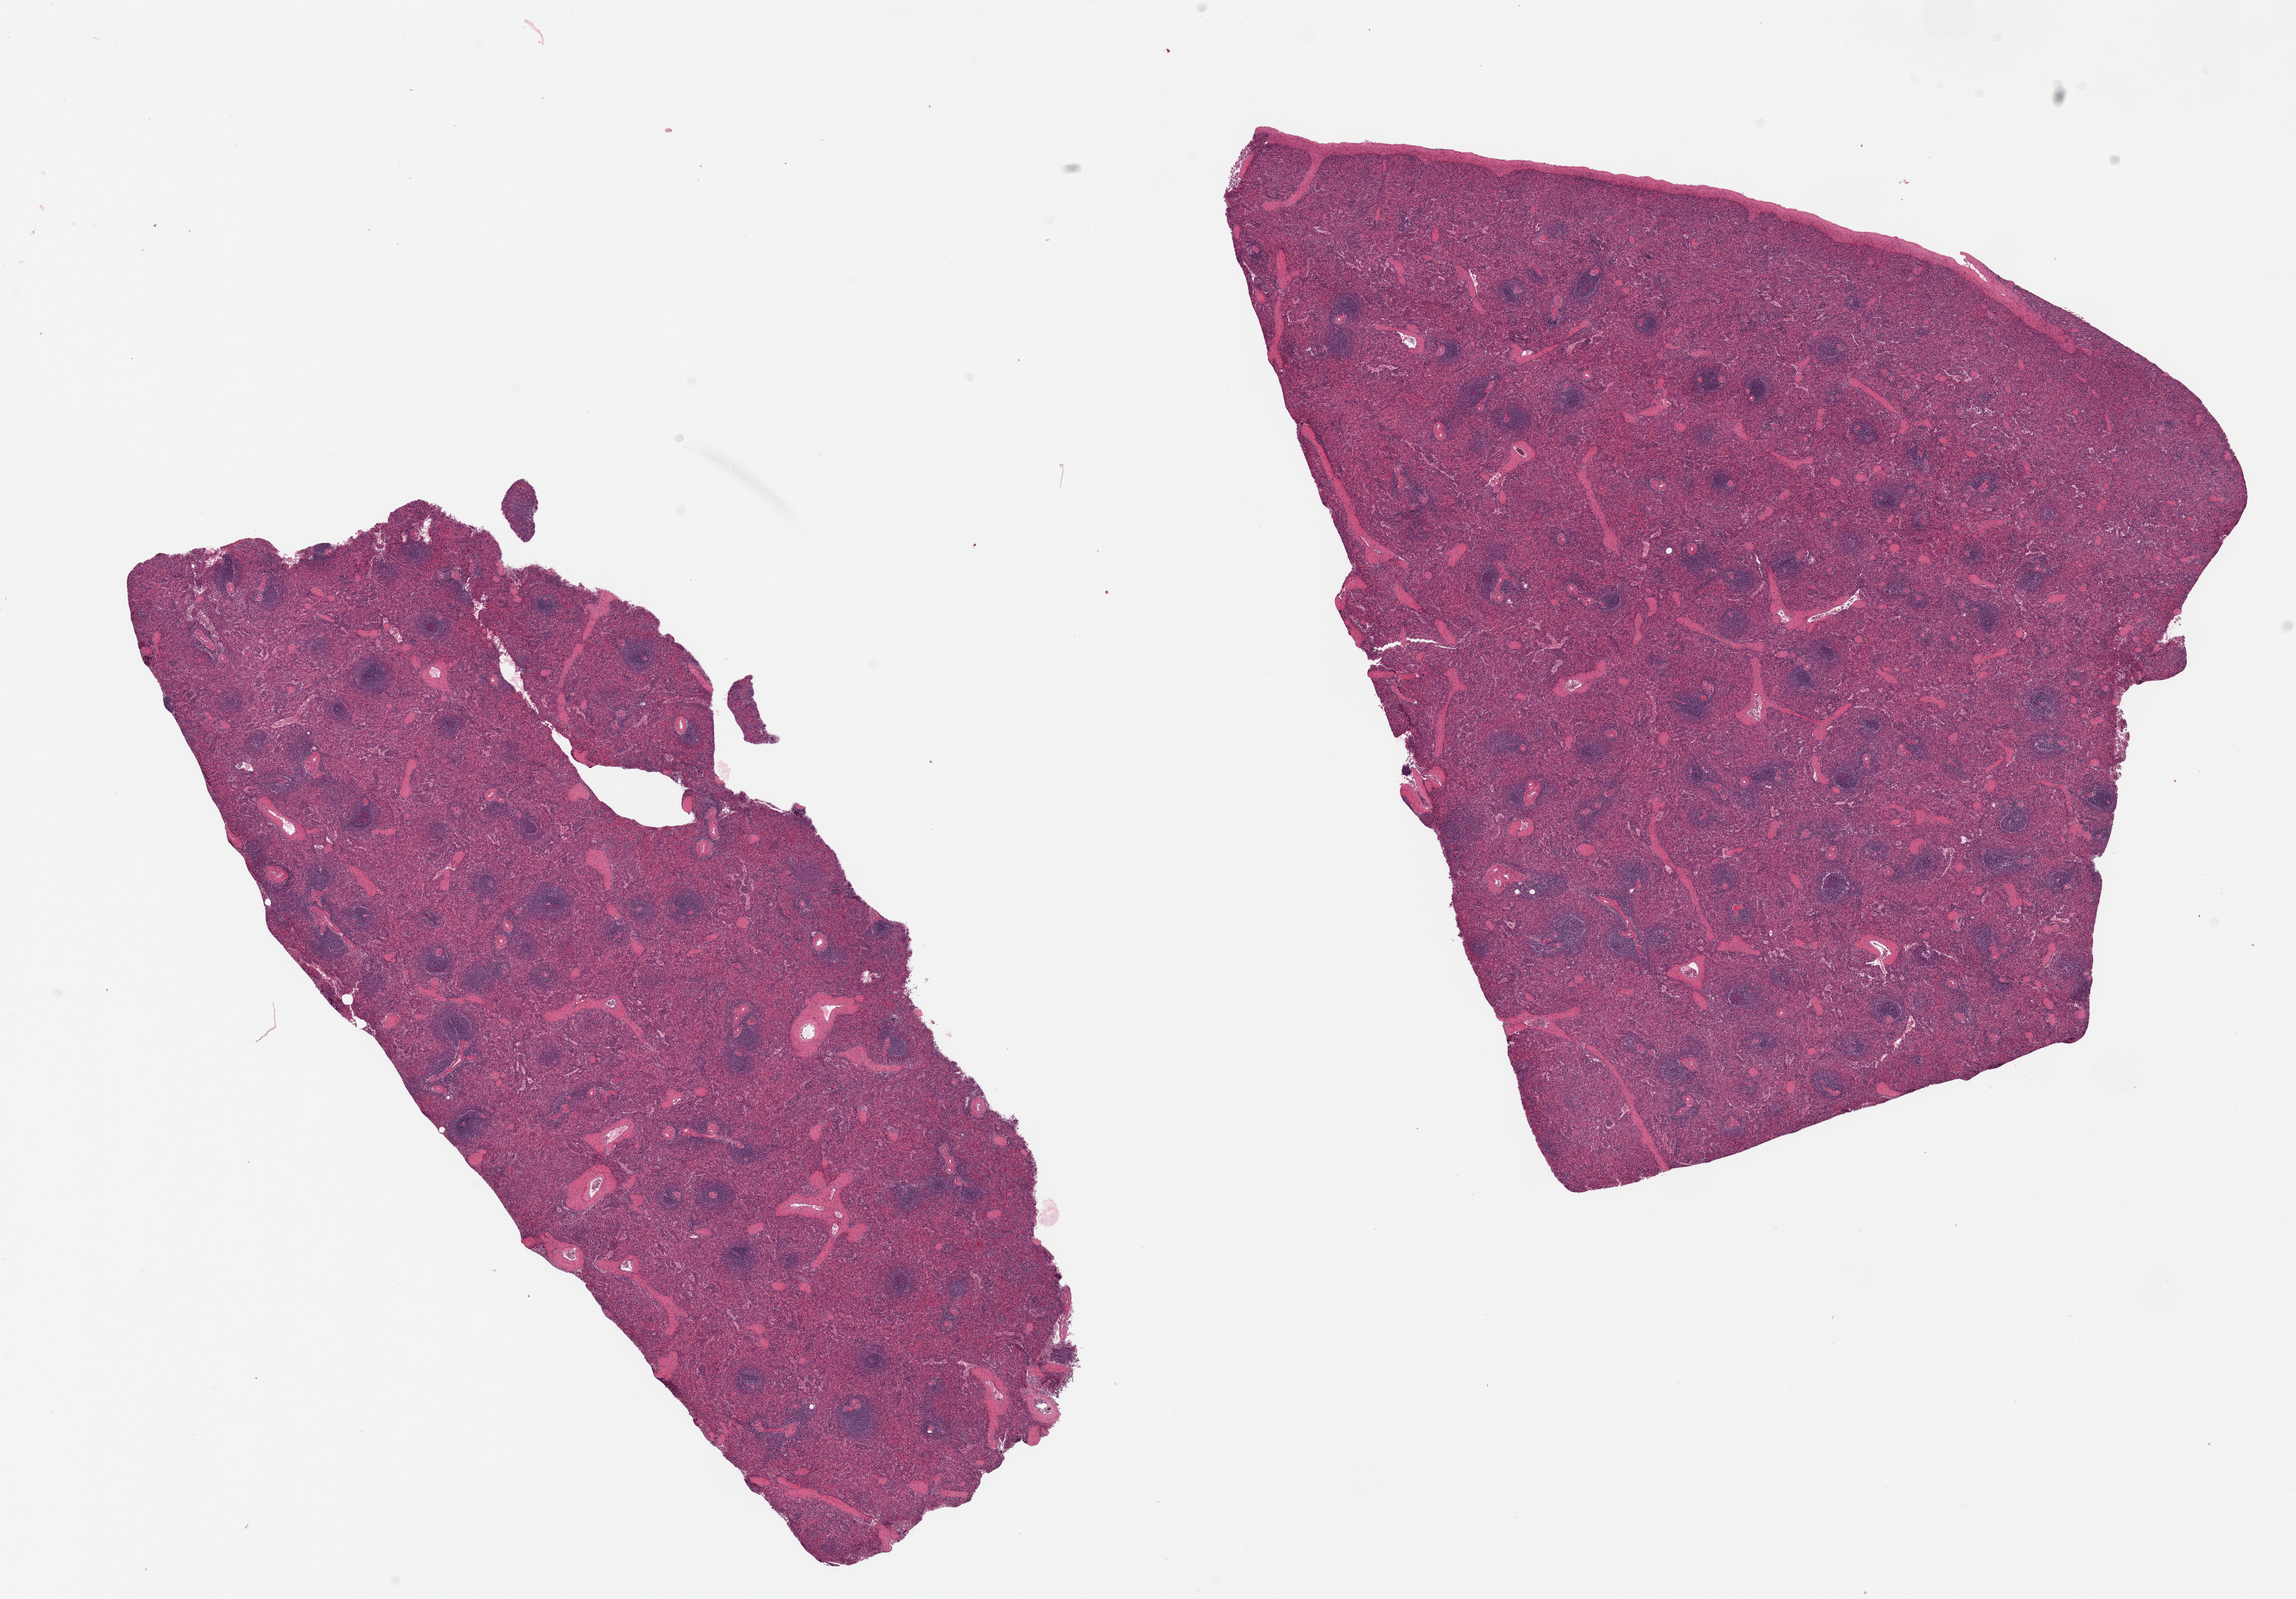
Digitized H&E-stained section — low-resolution overview of the scanned area, about 25.6 x 17.8 mm (from a 20x scan), PAXgene-fixed, paraffin-embedded tissue, section of spleen (target tissue), donor tissue sample.
Pathologist's review note for this sample: 2 pieces. Capsule present on larger piece; PLEASE sample beneath capsule.